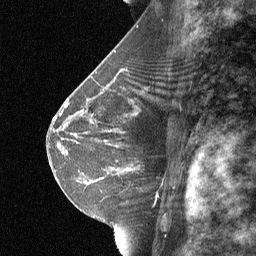
Breast MRI (dynamic contrast-enhanced), one sagittal slice. Slice 39 of 64 in the series (ordered by position). Dynamic contrast-enhanced study with each time point stored as its own series, time point 2 of 3 at this slice position (early post-contrast, ordered by acquisition time). 1.5 T. TE 4.8 ms, TR 27 ms. 2 mm slice thickness. 256 × 256 image matrix, field of view 180 × 180 mm. Patient: female, 42 years. From the clinical record (not read from this slice): setting: breast cancer imaged before/during neoadjuvant chemotherapy; receptor status: triple-negative.
Annotated regions visible in this slice (semi-automatic segmentation, software-assisted and operator-edited):
- analysis volume of interest (the breast-tissue region the enhancement analysis was run in; not a lesion): box from (x=99, y=117) to (x=174, y=187) px
- tumour enhancement mask (voxels above the 90 % enhancement threshold inside the analysis volume of interest): (x=113, y=168)–(x=129, y=170)